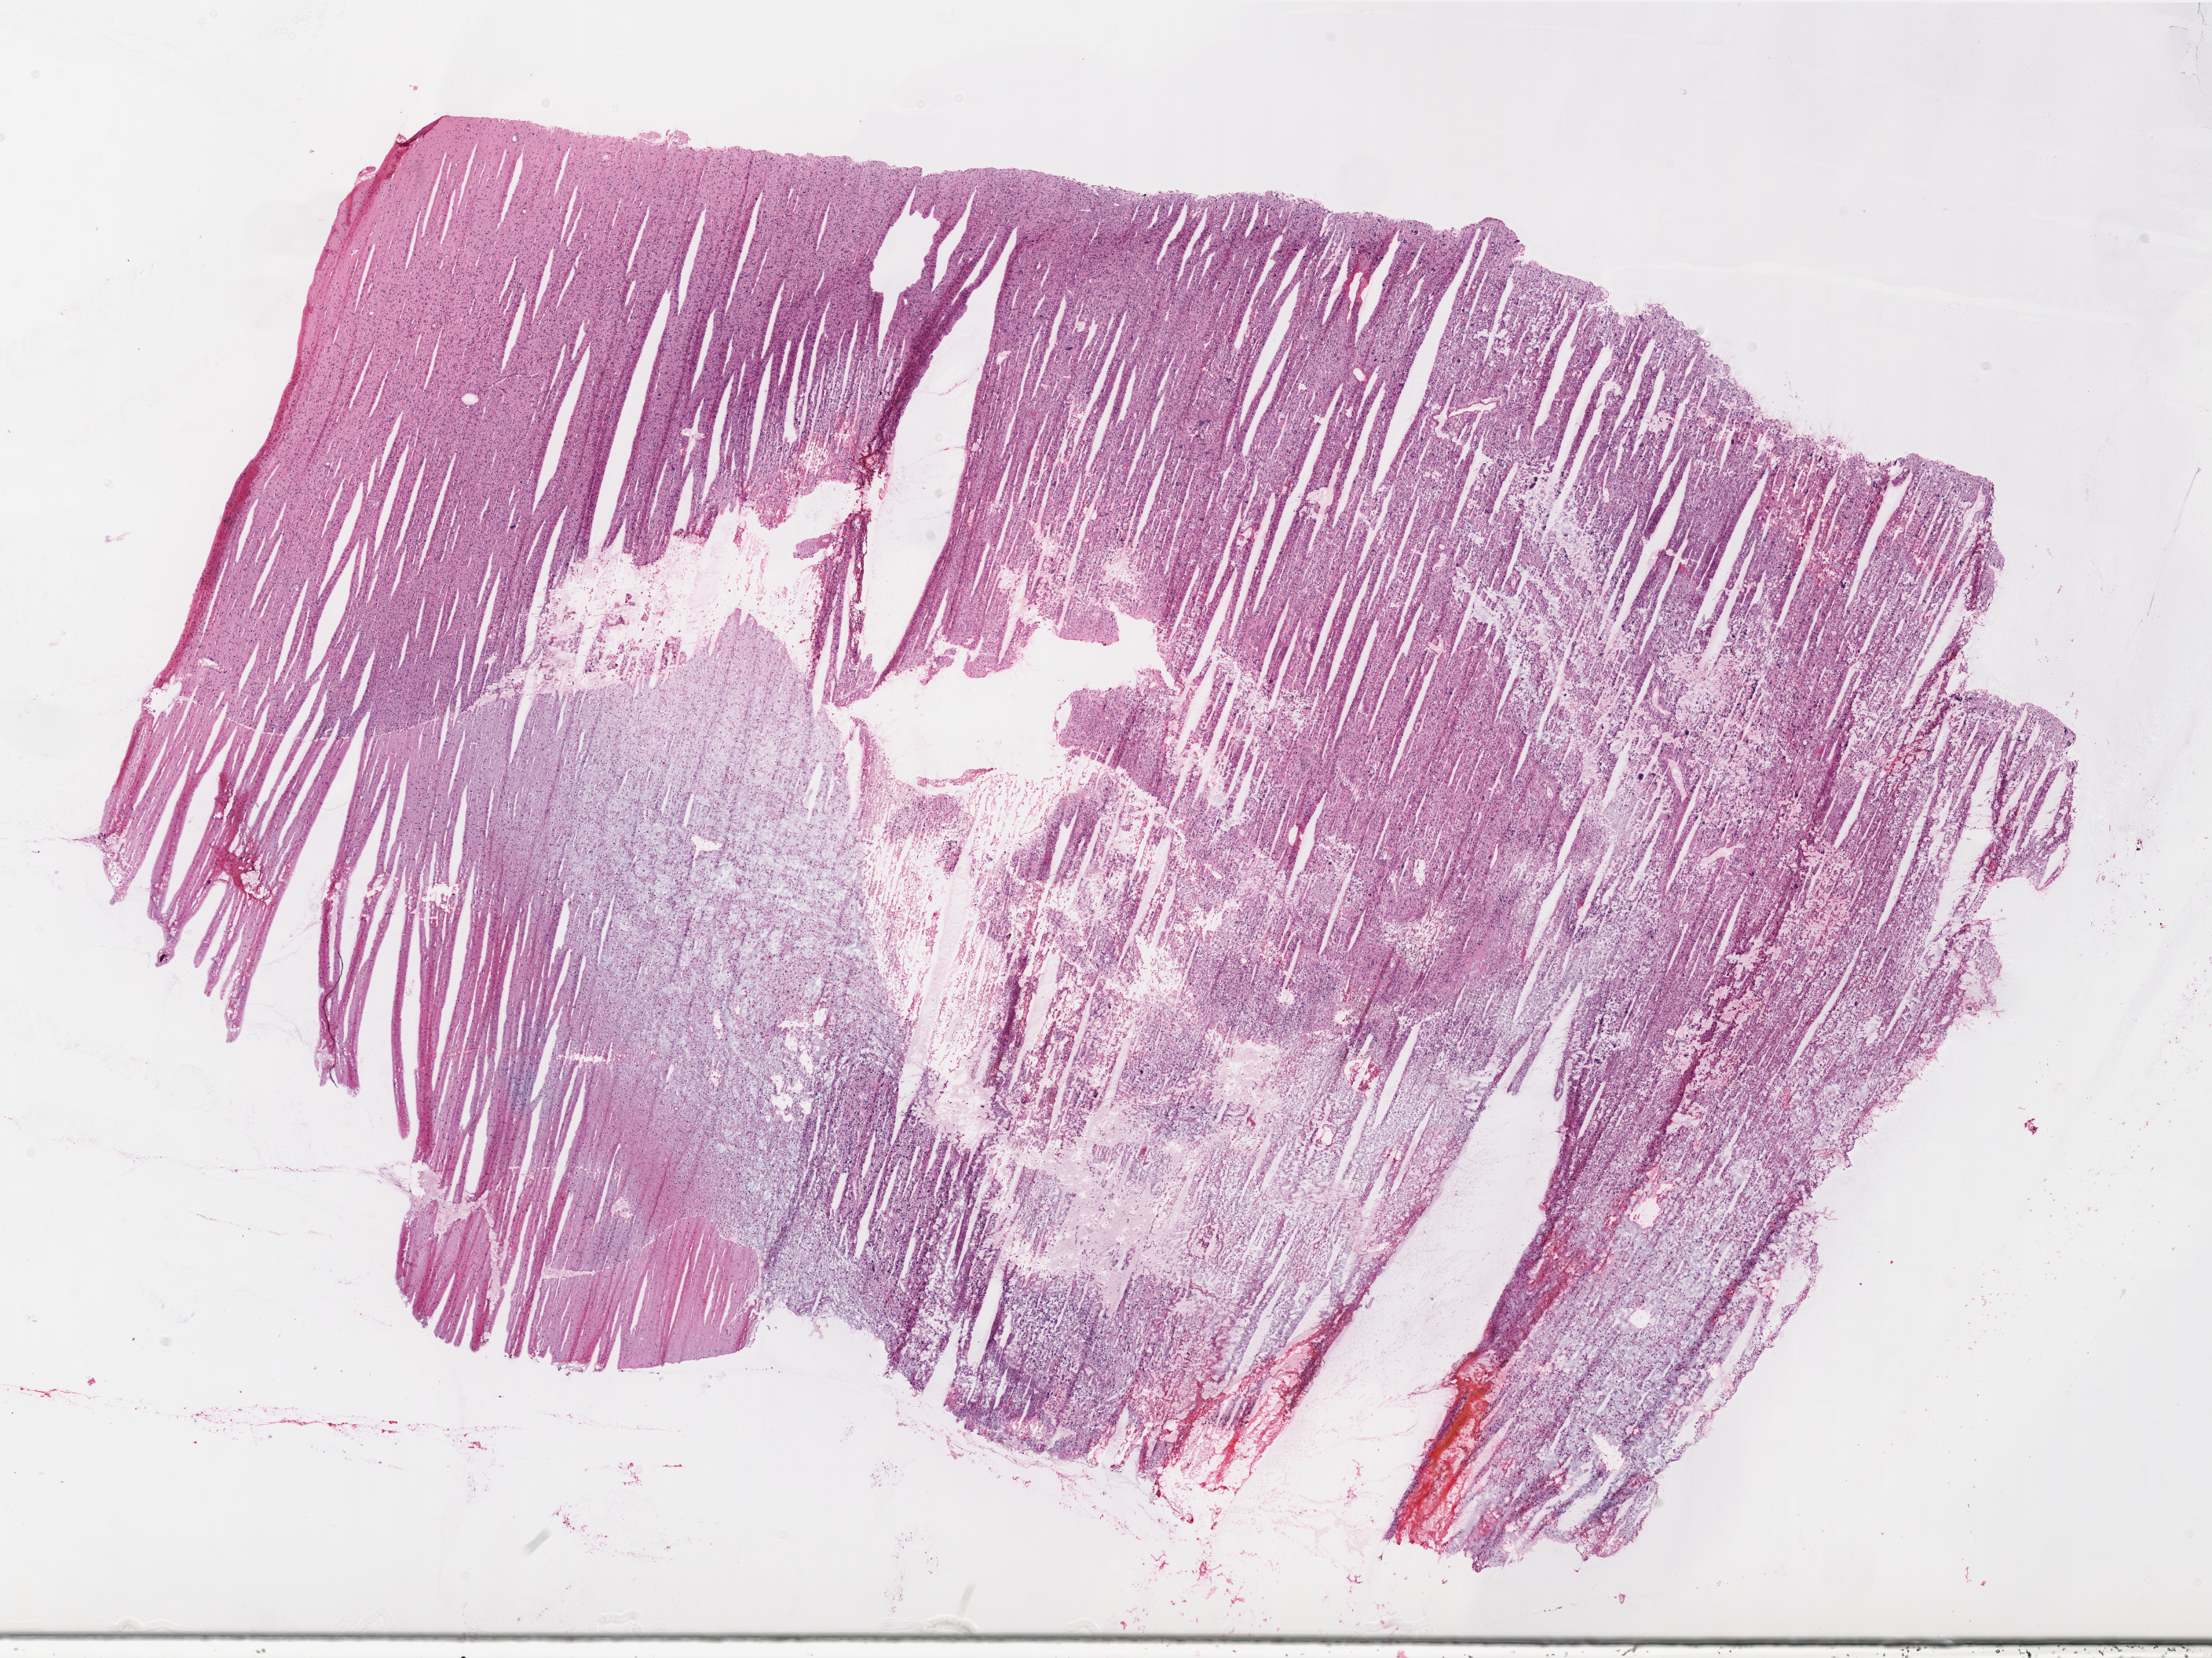
Digitized H&E tissue section (whole slide), a low-resolution overview of the entire scanned area, about 22.7 x 17.0 mm, frozen section from the top of the tissue portion, primary tumour sample from the brain. Female, age 66 years at initial diagnosis. Pathologist review of this section (percent, as recorded): tumour cells 60%, tumour nuclei 90%, normal cells 0%, stromal cells 20%, necrosis 20%.
* diagnosis: Glioblastoma